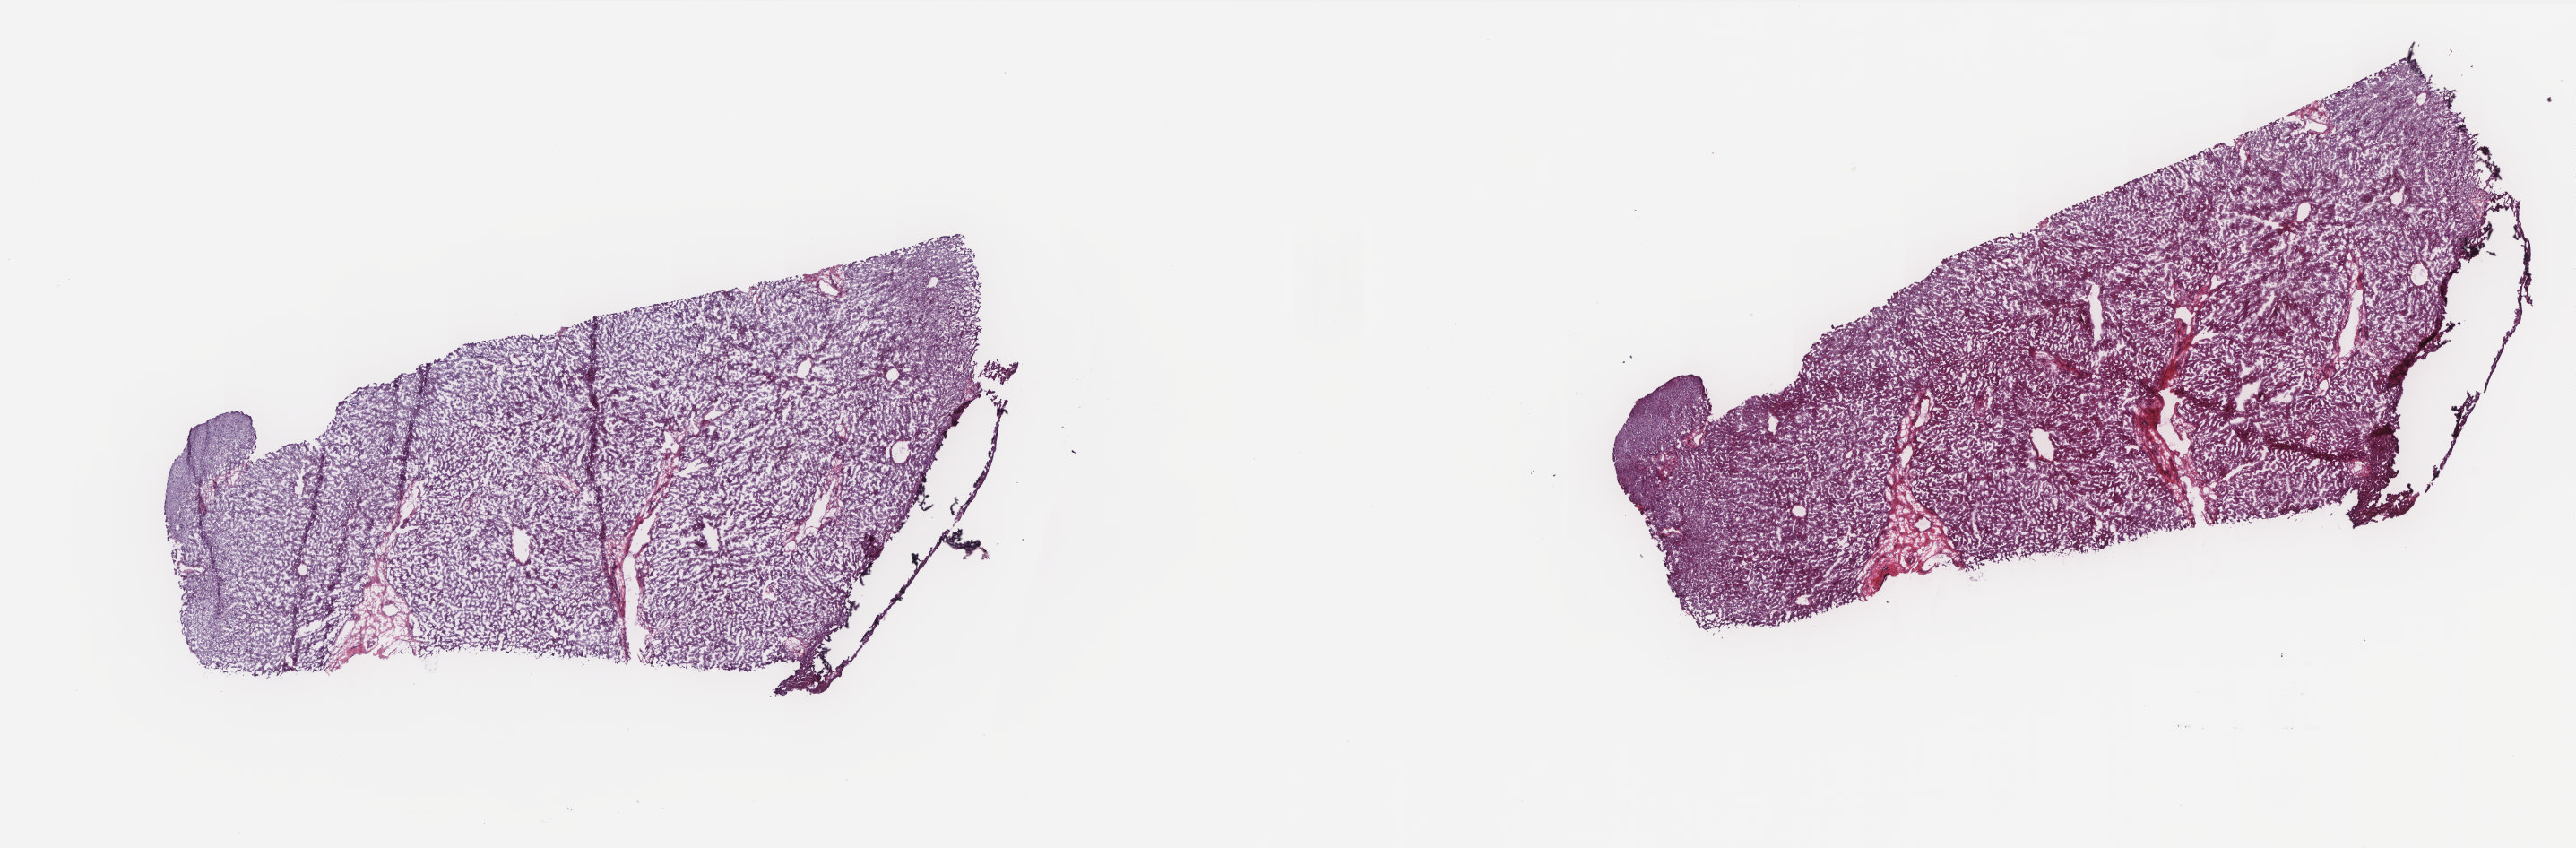
H&E whole-slide image, whole scanned area (about 23.0 x 7.6 mm) shown as a low-resolution overview. Frozen section from the top of the tissue portion. Liver, solid tissue normal (non-tumour tissue) sample. Patient: female, age at initial diagnosis 76 years. Pathologist review of this section (percent, as recorded): tumour cells 0%, tumour nuclei 0%, normal cells 100%, stromal cells 0%, necrosis 0%. Infiltration values recorded for this section: lymphocyte infiltration 1%, monocyte infiltration 0%, neutrophil infiltration 0%.
- this section: solid tissue normal (non-tumour) sample from the same patient
- patient diagnosis: Hepatocellular carcinoma, NOS